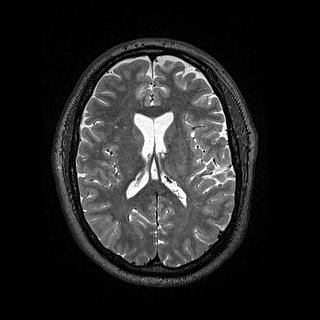
Brain MRI from a brain-tumour surgery series, one axial slice; slice 73 of 144 in the series (ordered by position); 1.2 mm slice thickness; 320 × 320 image matrix, field of view 254 × 254 mm. From the clinical record (not read from this slice): histopathology: Astrocytoma; WHO grade: 2.
Structures marked on this image (outlined manually by an expert reader):
- tumour: bounding box [x1, y1, x2, y2] px = [197, 159, 207, 169]